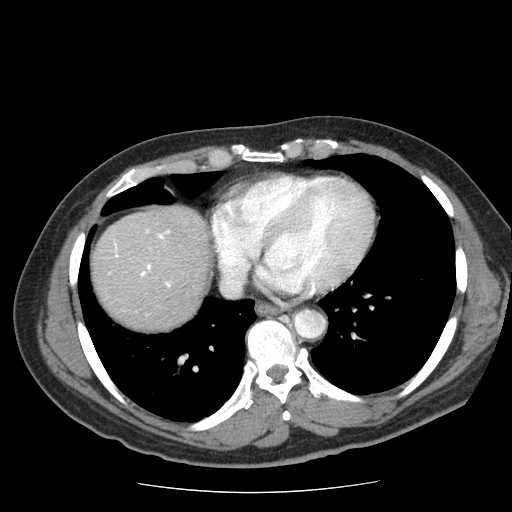
Contrast-enhanced abdominal CT (liver protocol), one axial slice; position 69 of 85 along the scan axis; reconstruction kernel STANDARD; 120 kVp; soft-tissue window (W 400 / L 40 HU); 2.5 mm slice thickness; 512 × 512 image matrix. Case-level facts recorded for this patient, not image findings: diagnosis: hepatocellular carcinoma (patient treated with transarterial chemoembolisation; whether this scan precedes or follows treatment is not stated here); TNM stage (as recorded): Stage-IIIA; Child-Pugh class: A; tumour differentiation: well differentiated; tumour nodularity: multinodular.
Outlined on this slice (semi-automatically segmented with operator editing):
- liver parenchyma outside the tumour (the mass and vessels are separate outlines, so this box may not span the whole liver): bounding box [x1, y1, x2, y2] px = [92, 206, 210, 330]
- liver vessels: [114, 230, 171, 287]